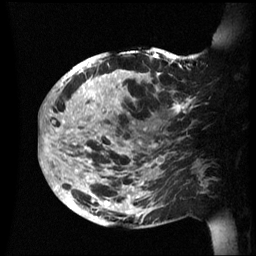
Breast MRI (dynamic contrast-enhanced), one sagittal slice. Position 24 of 60 along the scan axis. Dynamic contrast-enhanced series, image 2 of 3 at this slice position (ordered by acquisition). 1.5 T. TE 4.2 ms, TR 8.4 ms. 2.4 mm slice thickness. 256 × 256 image matrix, field of view 230 × 230 mm. Female patient, age 48 years.
Outlined on this slice (semi-automatic segmentation, software-assisted and operator-edited):
- analysis volume of interest (the breast-tissue region the enhancement analysis was run in; not a lesion): bounding box (x1, y1, x2, y2) in pixels: (42, 47, 202, 229)
- tumour enhancement mask (voxels above the 70 % enhancement threshold inside the analysis volume of interest): (42, 50, 187, 218)